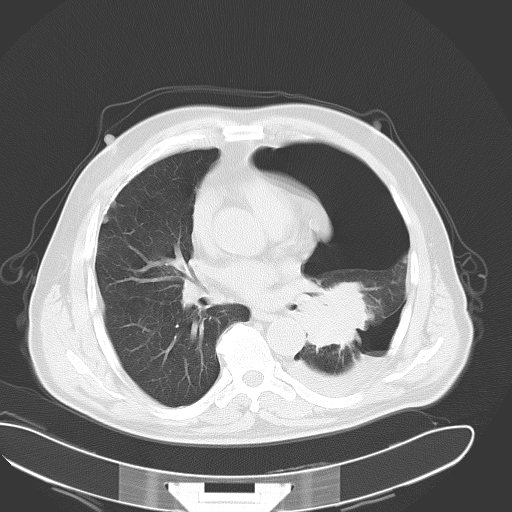
Chest CT, one axial slice. Slice 23 of 43 in the series (ordered by position). Reconstruction kernel B70f. 120 kVp. Lung window (W 1500 / L -600 HU). 8 mm slice thickness. 512 × 512 image matrix, field of view 418 × 418 mm. Male patient, age 62 years. From the clinical record (not read from this slice): clinical TNM (as recorded): T3 N0 M1.
Annotated regions visible in this slice (bounding box drawn by a radiologist):
- lung tumour (recorded histology: adenocarcinoma): bounding box (x1, y1, x2, y2) in pixels: (295, 281, 374, 350)
- lung tumour (recorded histology: adenocarcinoma): (303, 283, 369, 349)